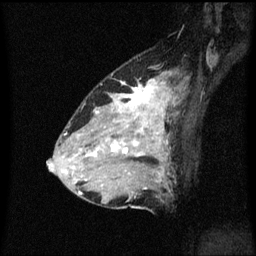
Breast MRI (dynamic contrast-enhanced), one sagittal slice; slice 38 of 60 in the series (ordered by position); dynamic contrast-enhanced series, image 2 of 3 at this slice position (ordered by acquisition); 1.5 T; TE 4.2 ms, TR 8.4 ms; 2 mm slice thickness; 256 × 256 image matrix, field of view 200 × 200 mm. Female patient, age 34 years. From the clinical record (not read from this slice): setting: breast cancer imaged before/during neoadjuvant chemotherapy; receptor status: HR-positive, HER2-negative.
Structures marked on this image (semi-automatic segmentation, software-assisted and operator-edited):
- analysis volume of interest (the breast-tissue region the enhancement analysis was run in; not a lesion): bounding box <69,72,178,209> (left, top, right, bottom; pixels)
- tumour enhancement mask (voxels above the 70 % enhancement threshold inside the analysis volume of interest): <79,80,170,195>